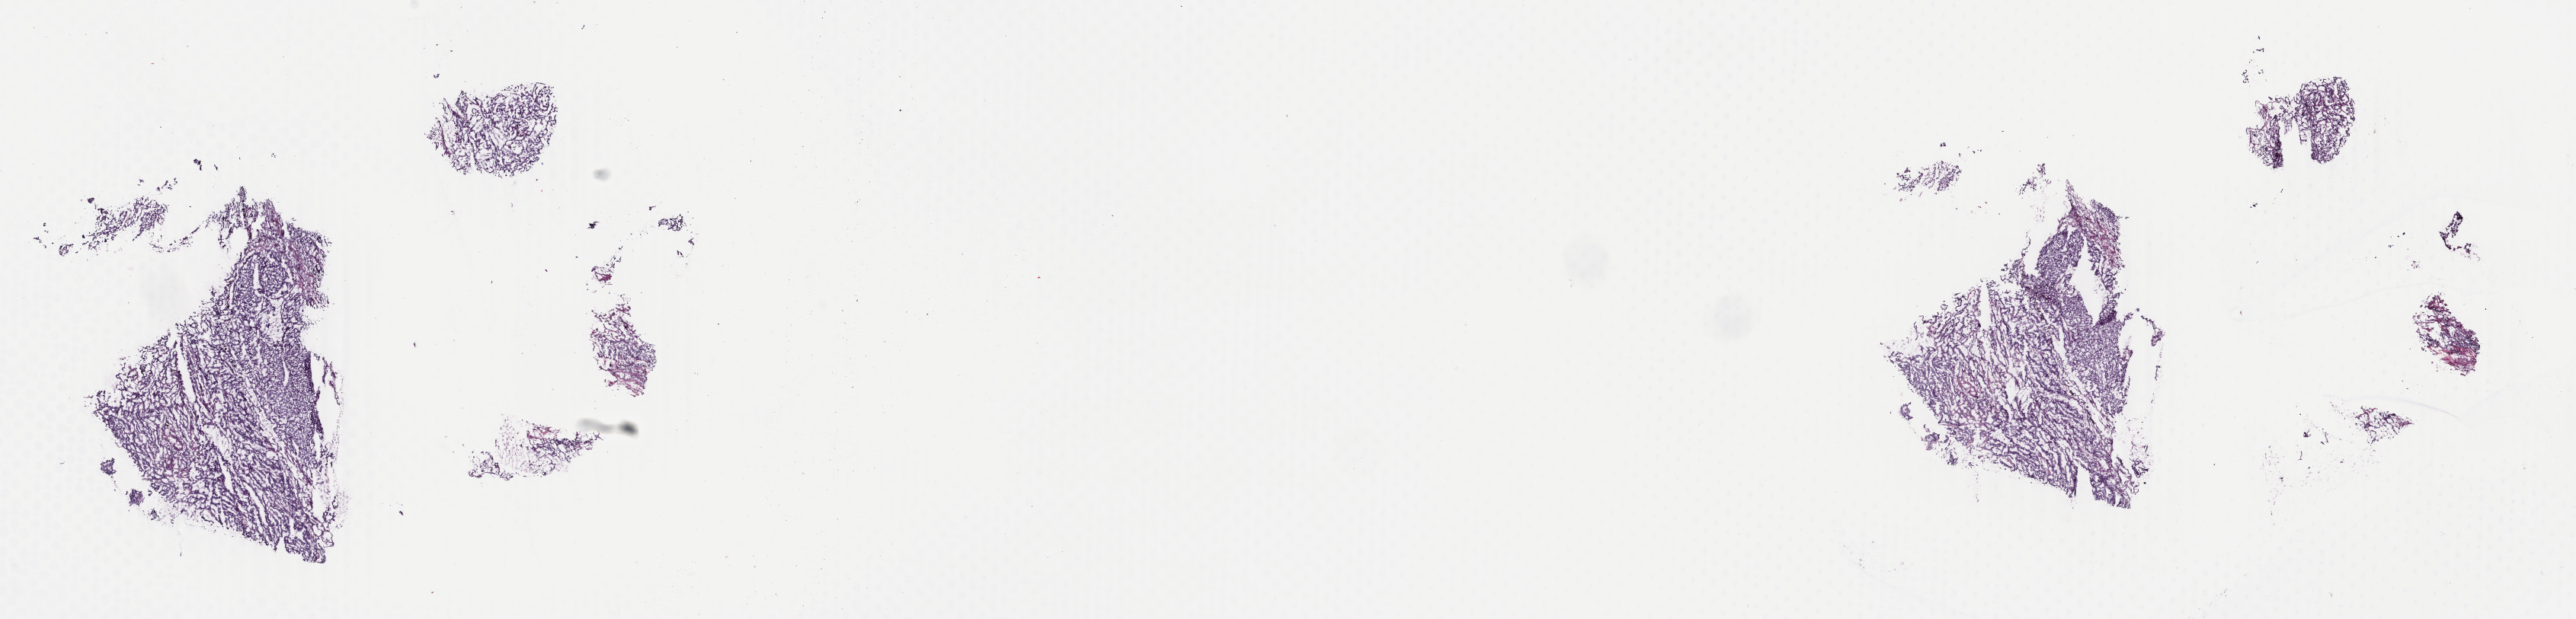
Whole-slide histology image, H&E, whole scanned area (about 26.9 x 6.5 mm, slide scanned at 40x) shown as a low-resolution overview; frozen section from the top of the tissue portion; primary tumour sample from the lung. Patient: female, age at initial diagnosis 48 years. Slide review estimates, as recorded: tumour cells 100%, tumour nuclei 80%.
Histologic diagnosis: Adenocarcinoma, NOS (upper lobe, lung).